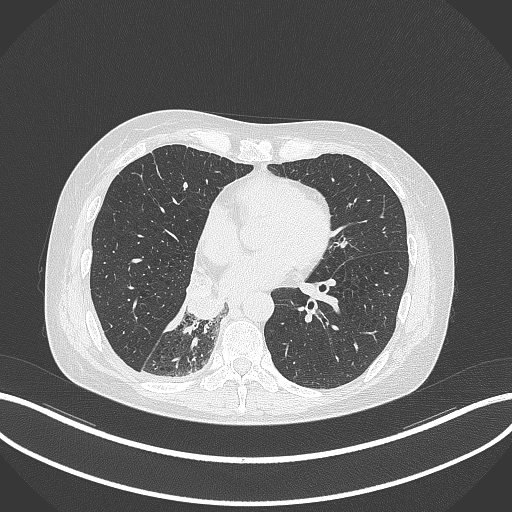
Chest CT, one axial slice. Reconstruction kernel B70f. Lung window (W 1500 / L -600 HU). 512 × 512 image matrix, field of view 400 × 400 mm. Patient: female, 63 years. From the clinical record (not read from this slice): clinical TNM (as recorded): T1c N0 M0.
Structures marked on this image (bounding box drawn by a radiologist):
- lung tumour (recorded histology: adenocarcinoma): bounding box (x1, y1, x2, y2) in pixels: (179, 270, 228, 324)